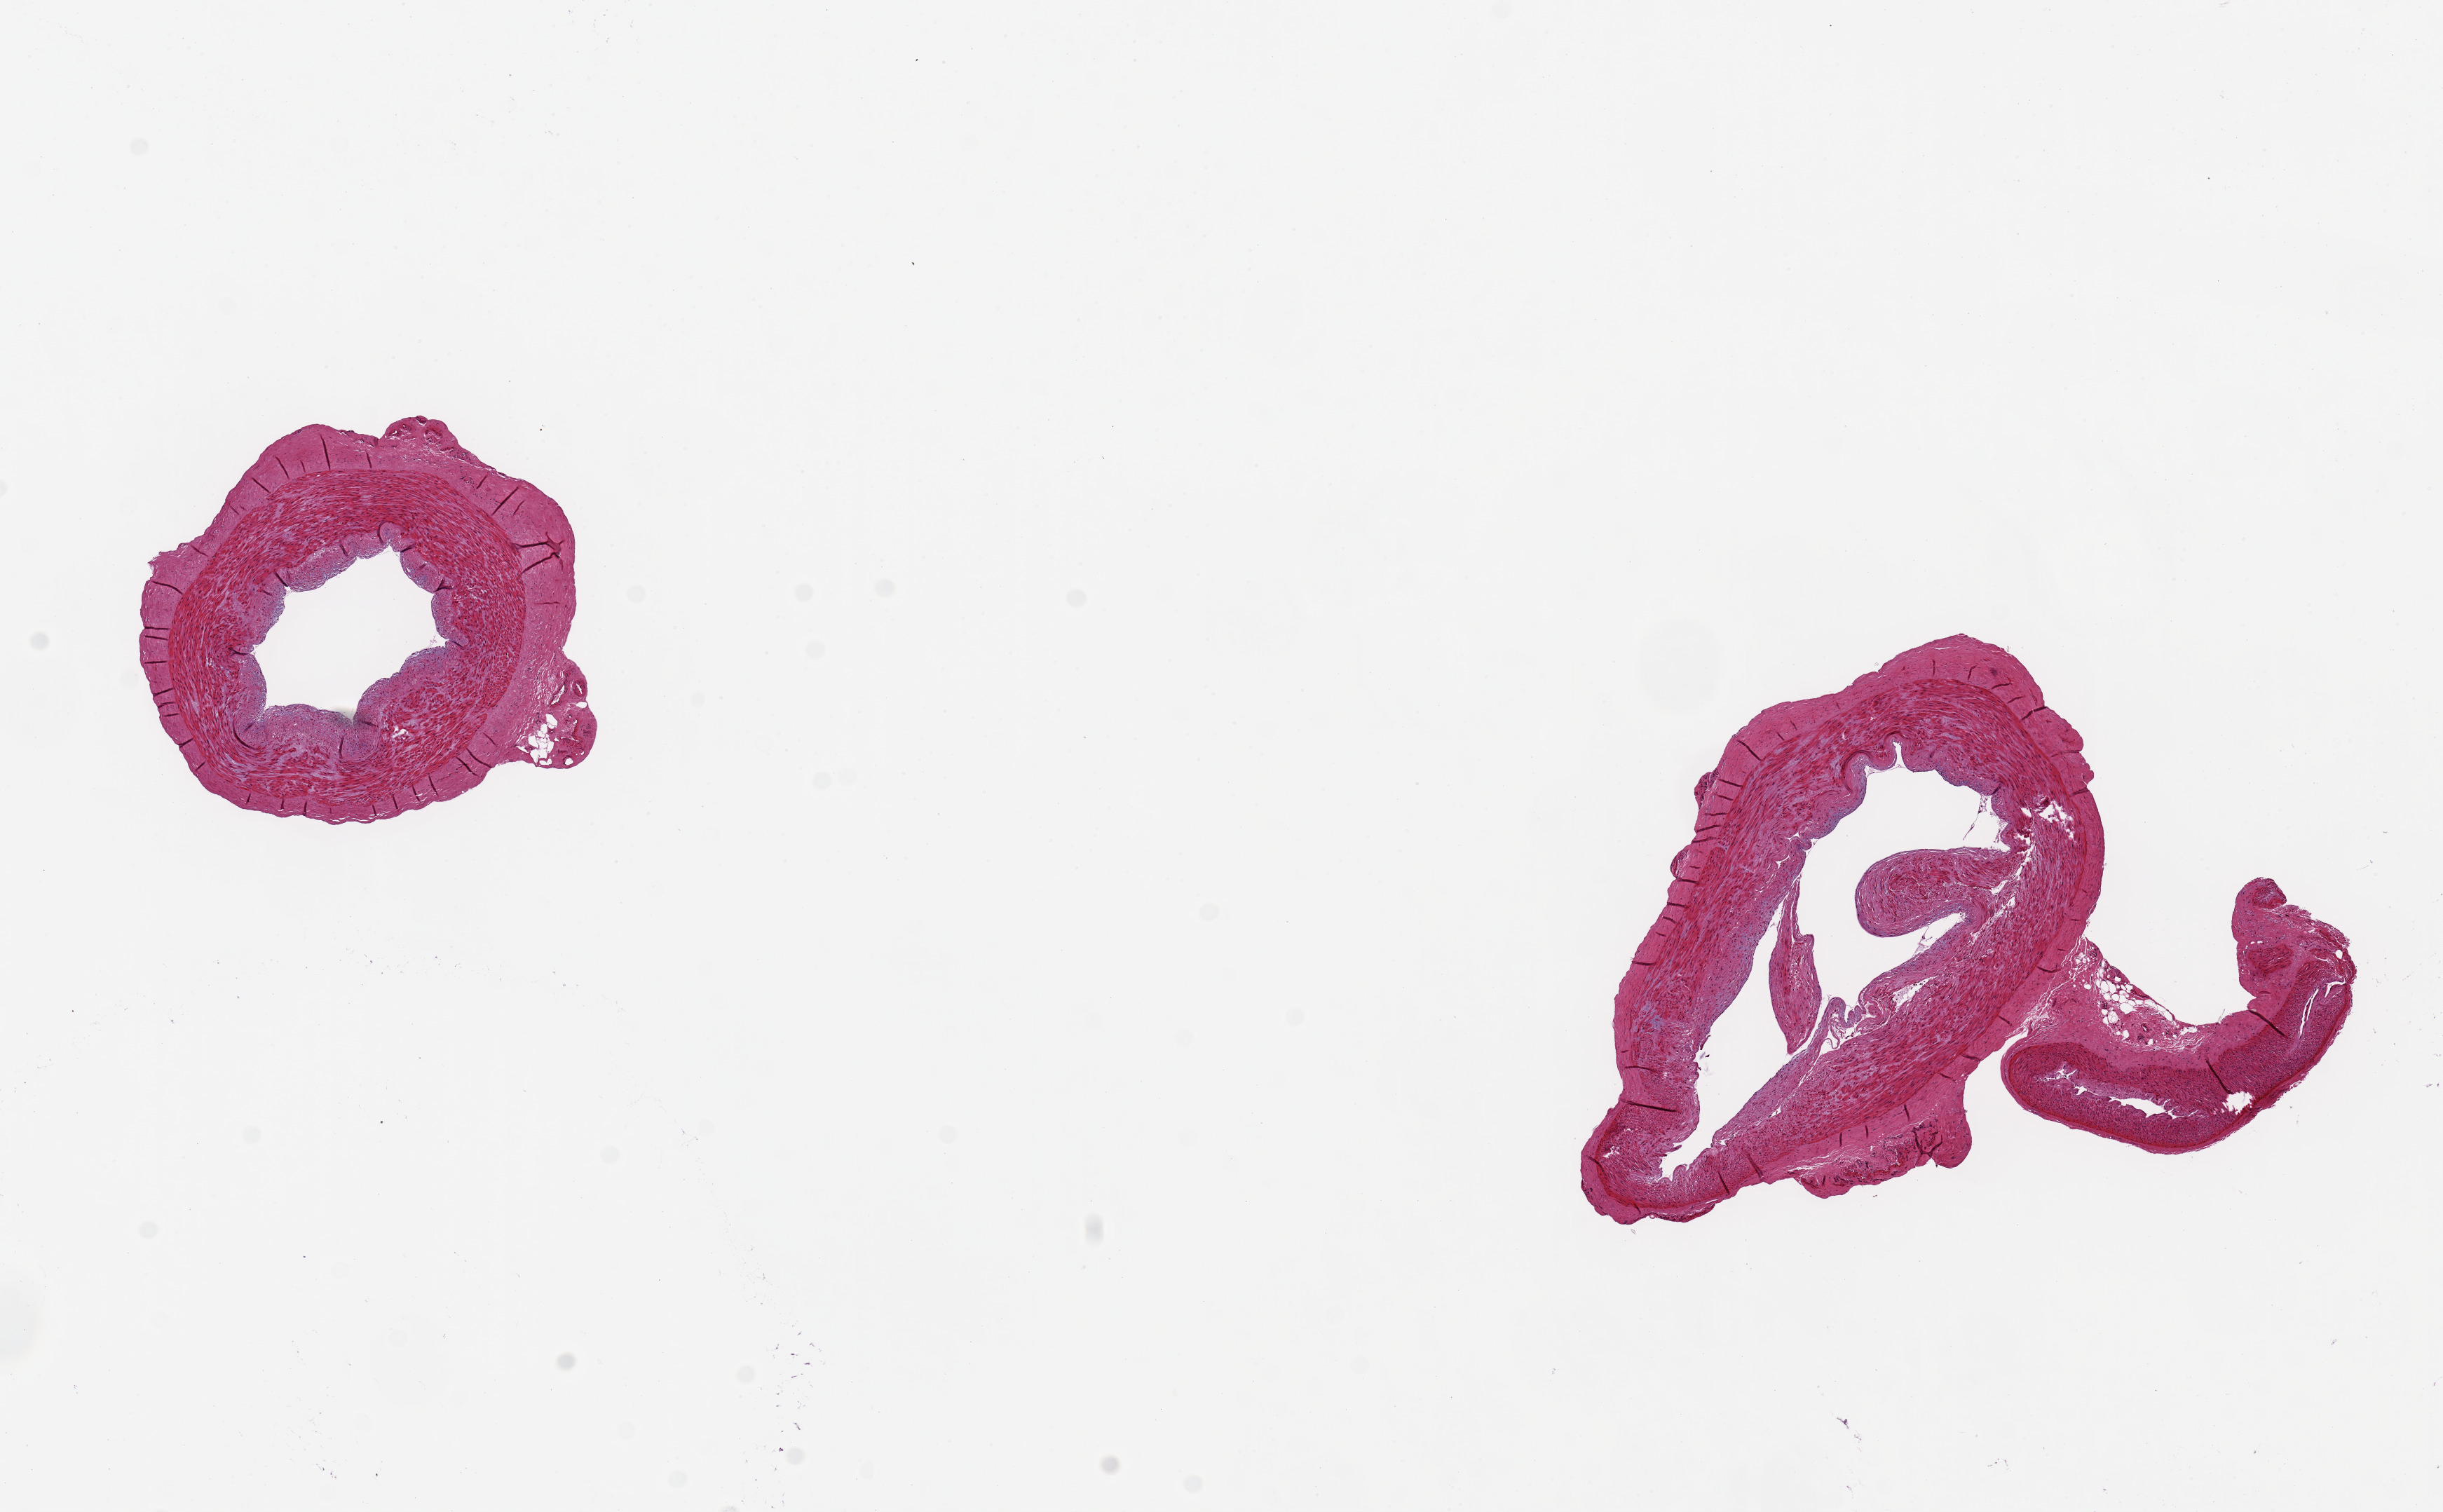
Hematoxylin and eosin (H&E) whole-slide image, brightfield — shown as a low-resolution overview of the whole scanned area (about 13.8 x 8.5 mm), PAXgene-fixed, paraffin-embedded tissue, target tissue: tibial artery, donor tissue sample. Donor: male.
Review note (as recorded): 2 pieces, 3x2 & 4x4mm; intimal fibrosis 0.2 mm; minimal external adipose.